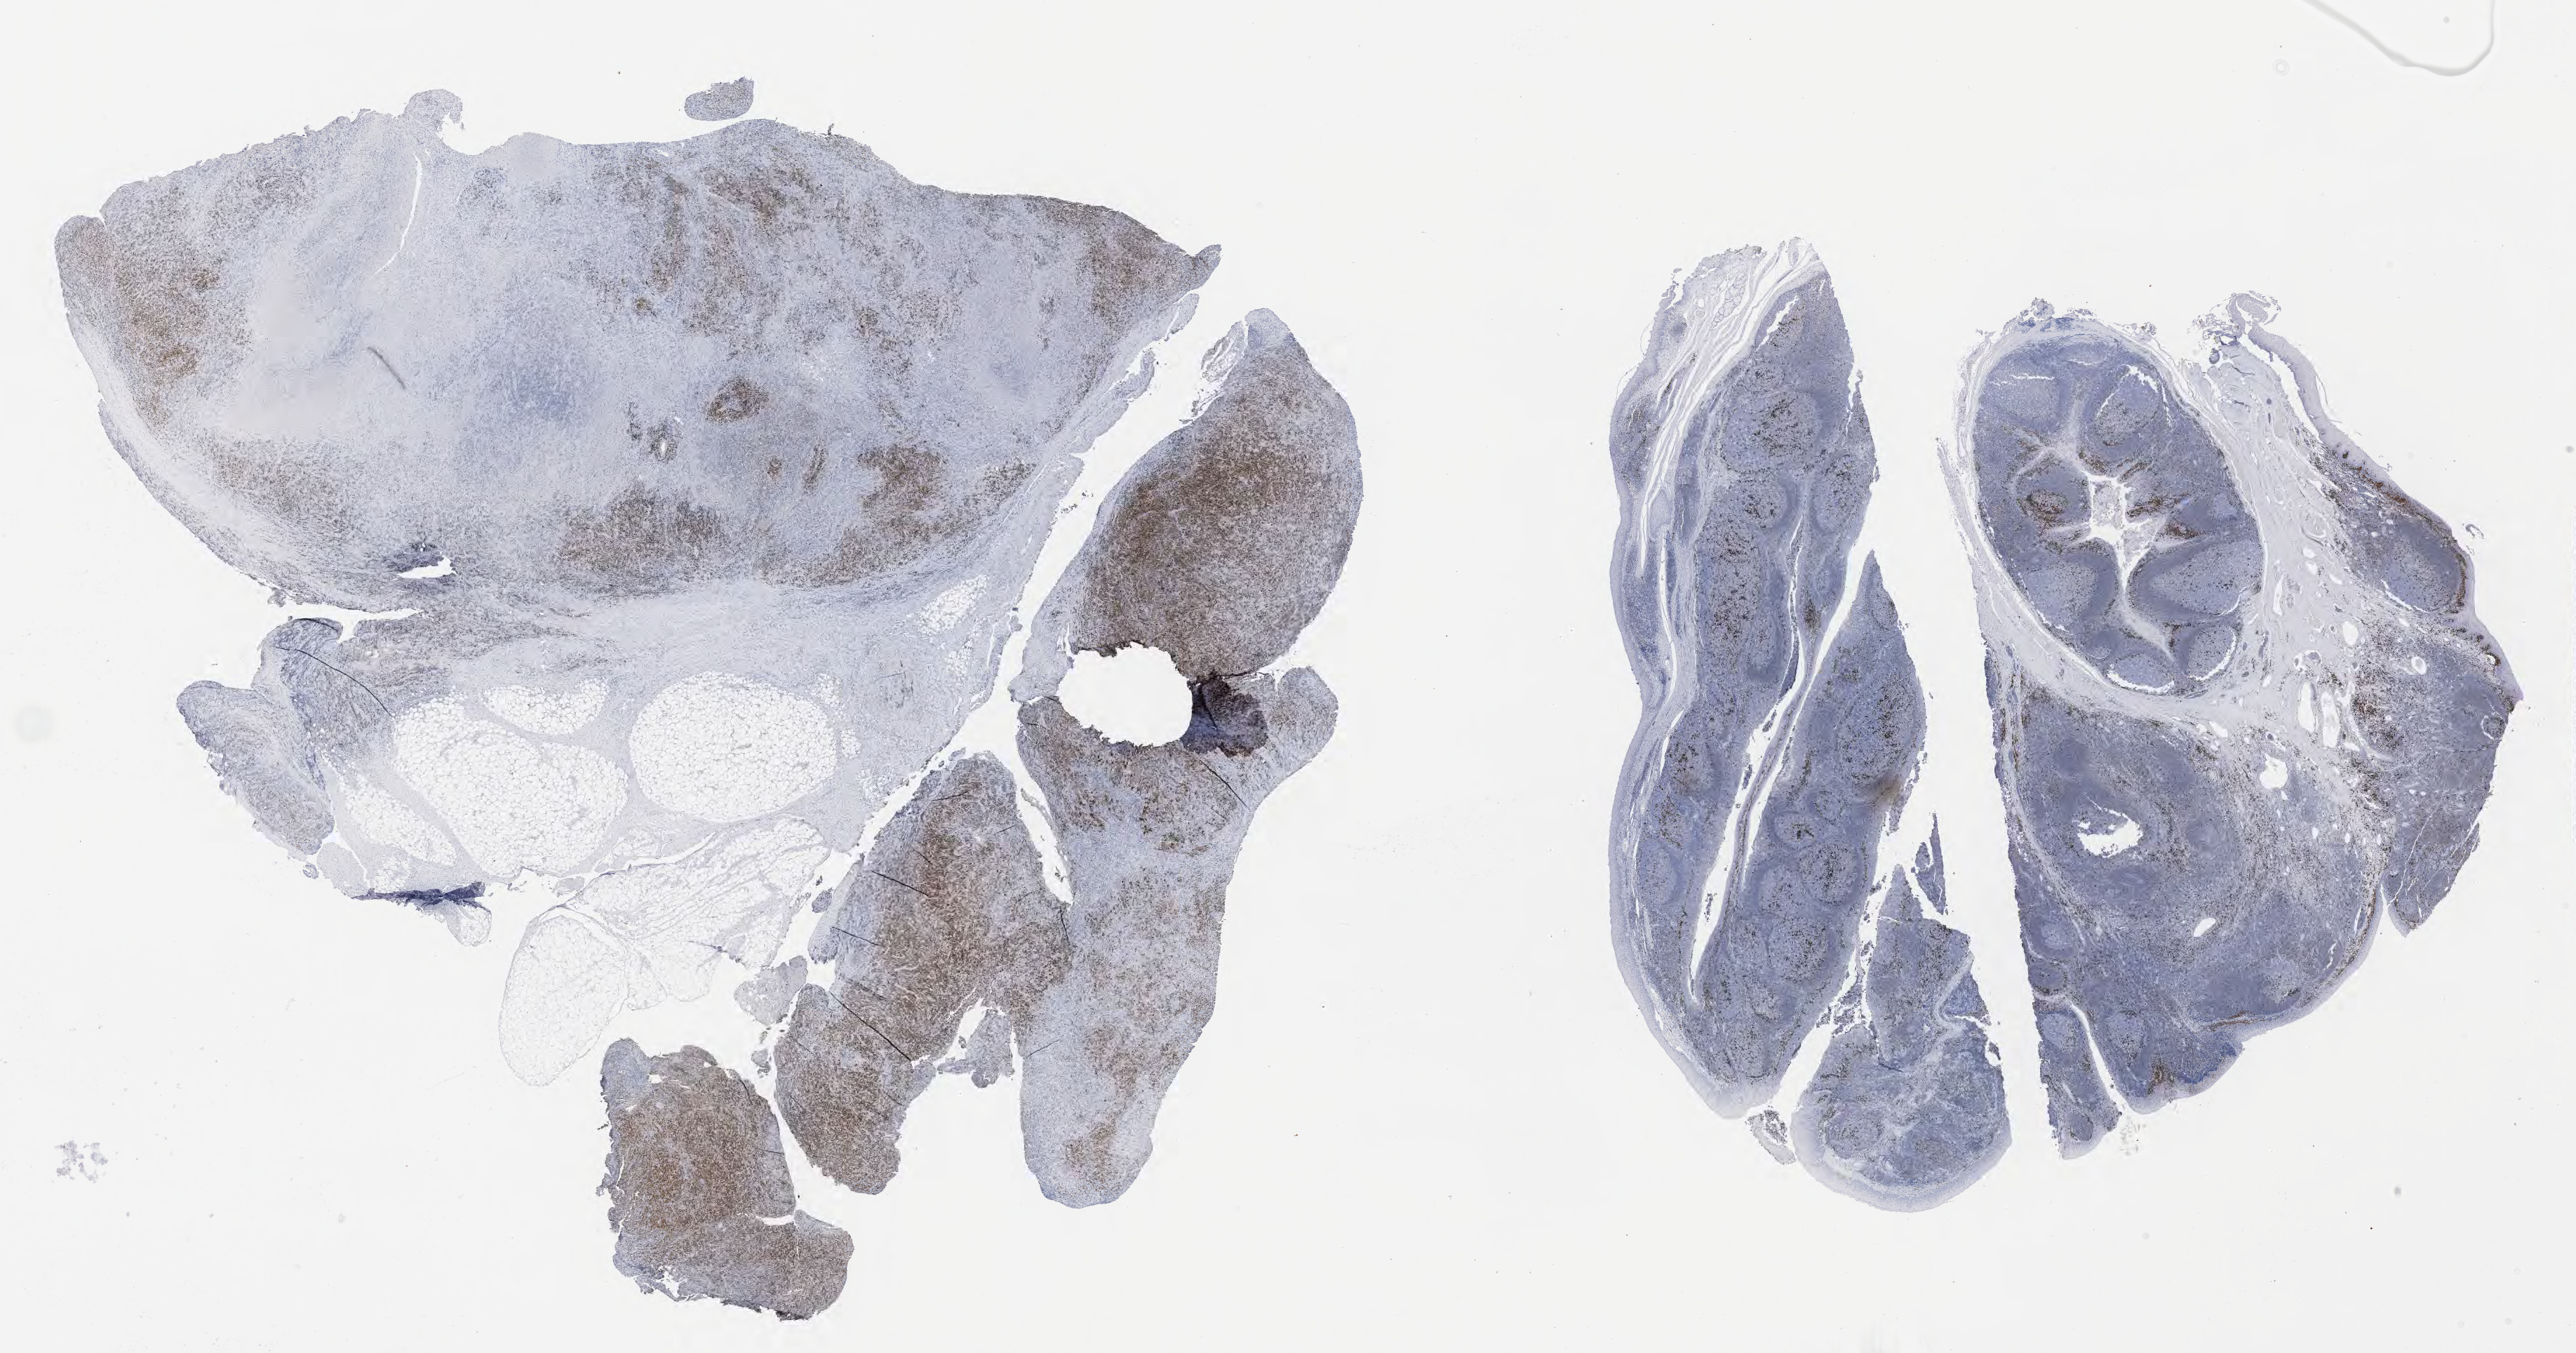
Whole-slide image, immunohistochemical stain for IRF4/MUM1 — whole scanned area (about 29.7 x 15.6 mm) shown as a low-resolution overview. Tumor tissue. Patient: female, age 46 years.
- diagnosis: Diffuse large B-cell lymphoma, NOS